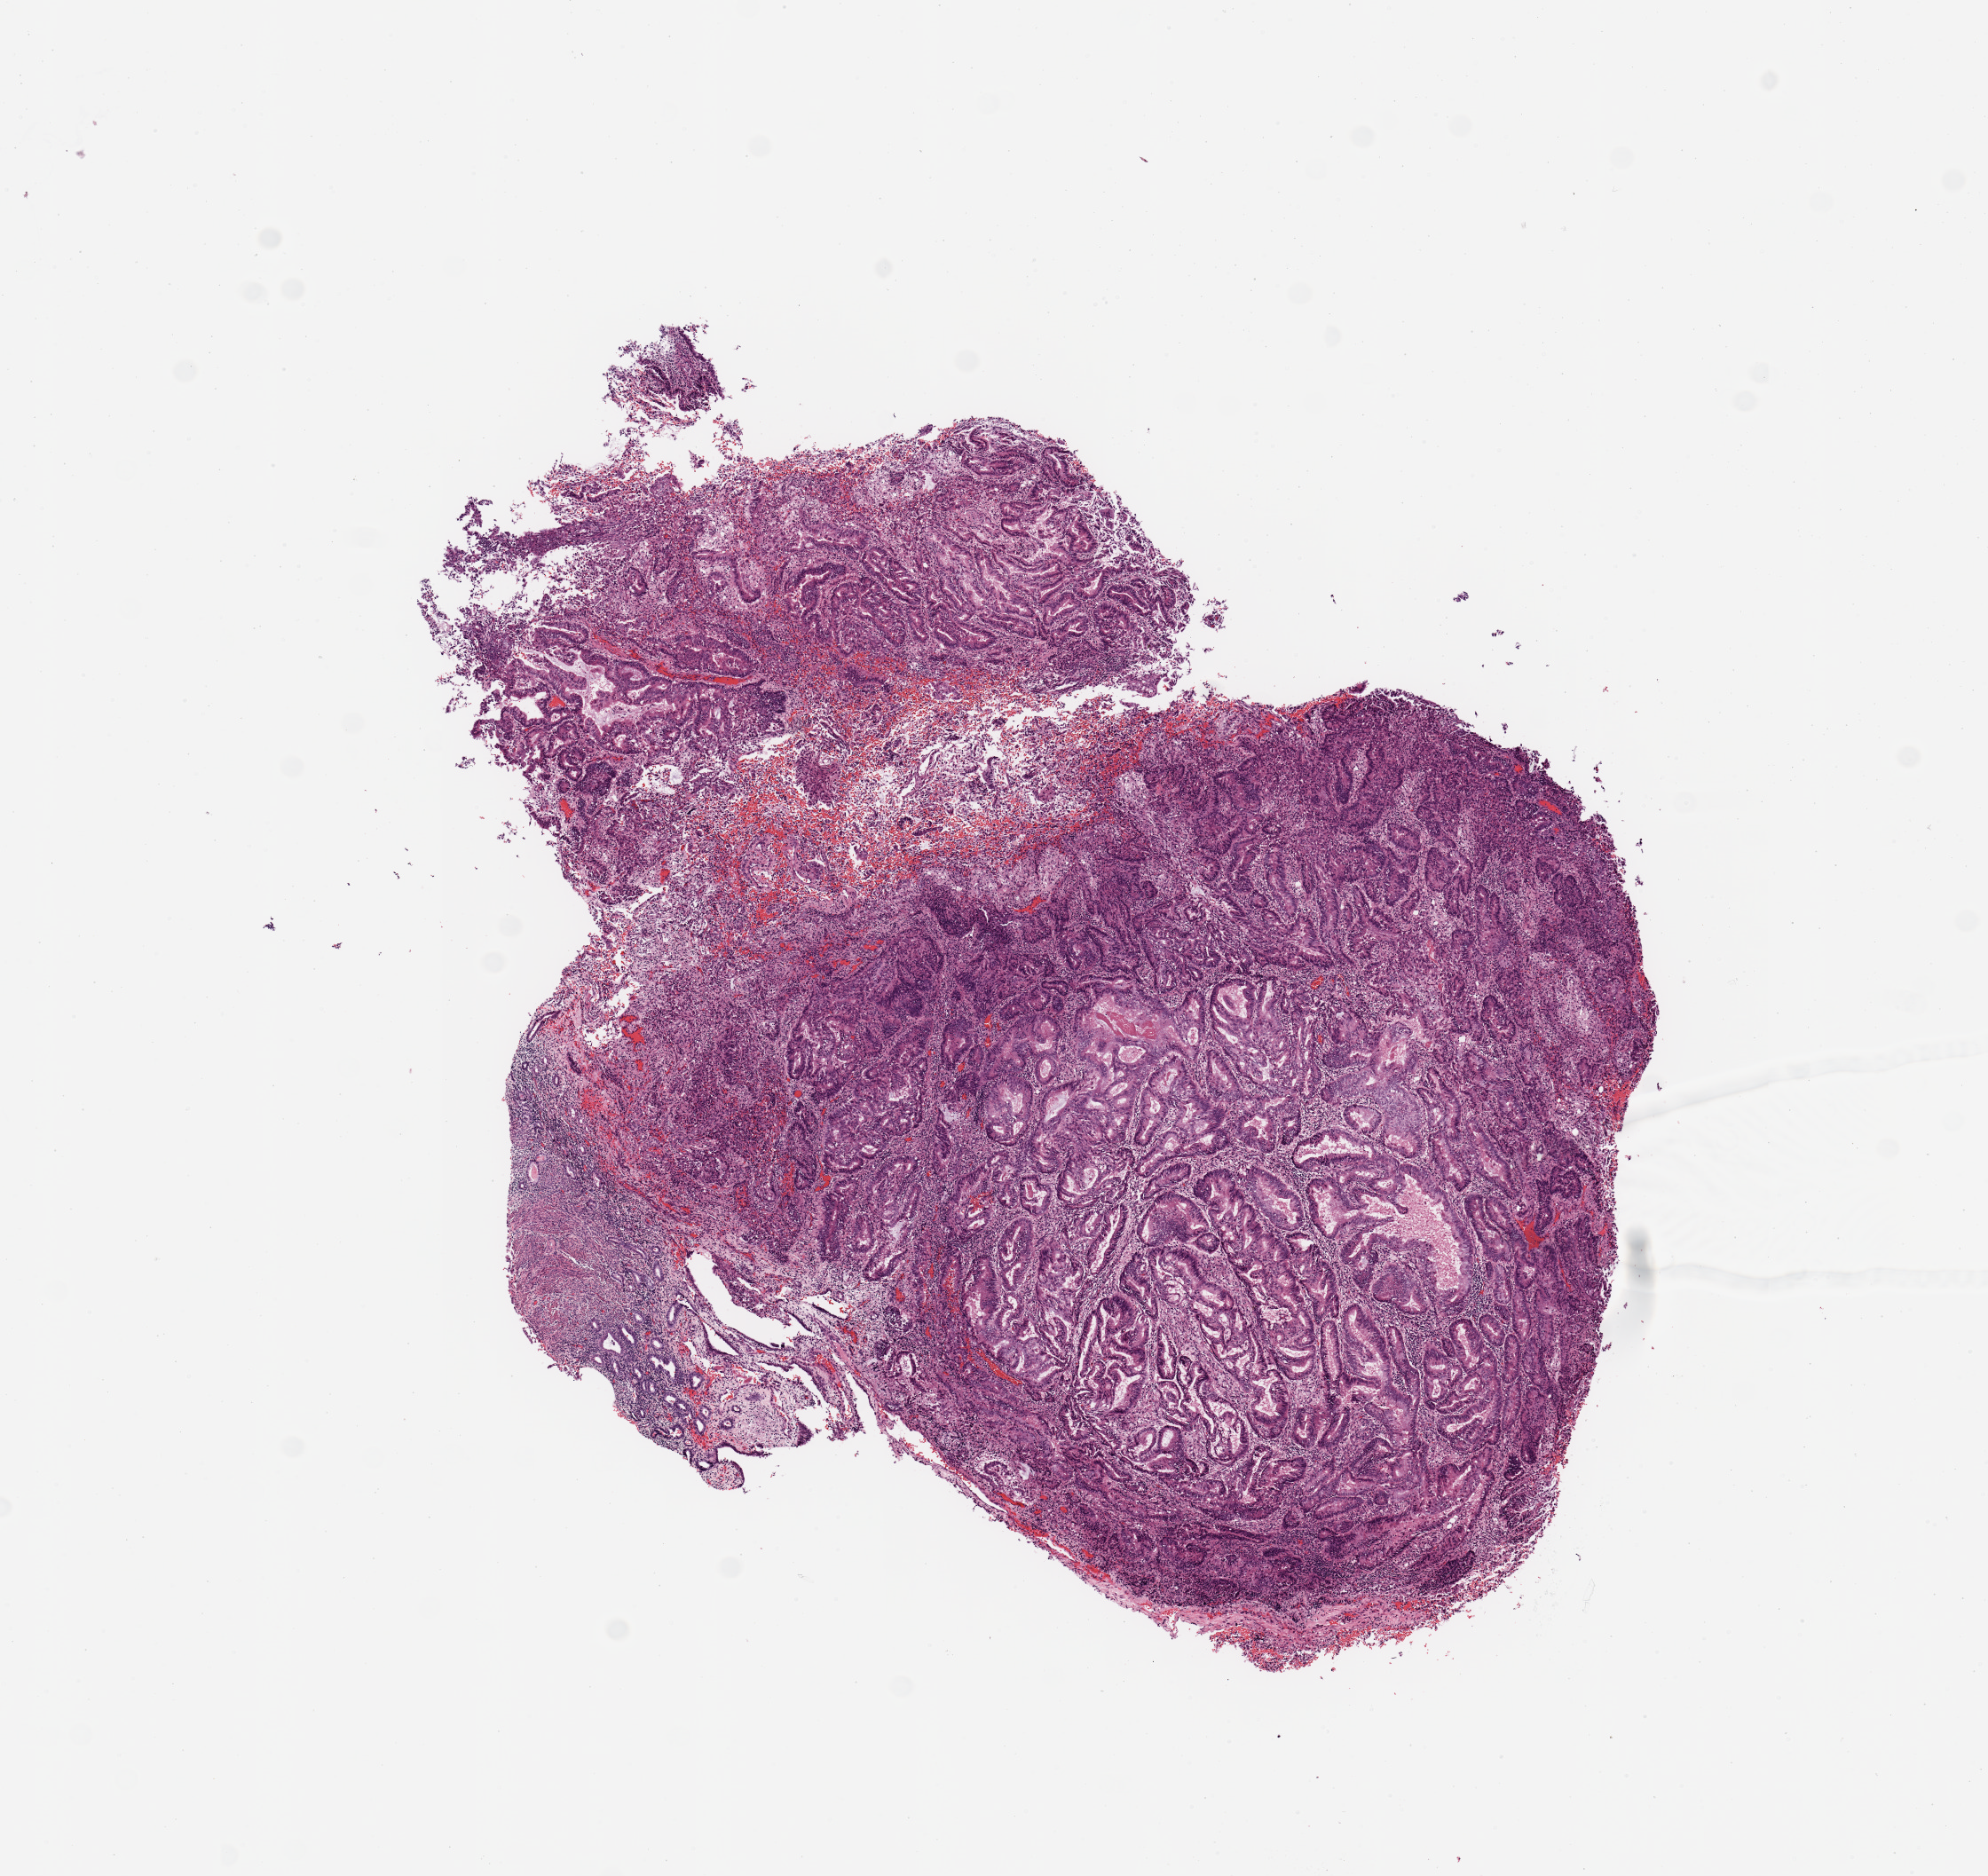
Whole-slide histology image, H&E-stained — whole scanned area (about 8.9 x 8.4 mm, acquisition: 20x scan) shown as a low-resolution overview, tumour tissue sample, uterus. 56-year-old female patient. Histologic grade: G1 (well differentiated).
* AJCC pathologic stage: I
* primary tumour site (as recorded): anterior endometrium
* diagnosis: Endometrioid adenocarcinoma, NOS